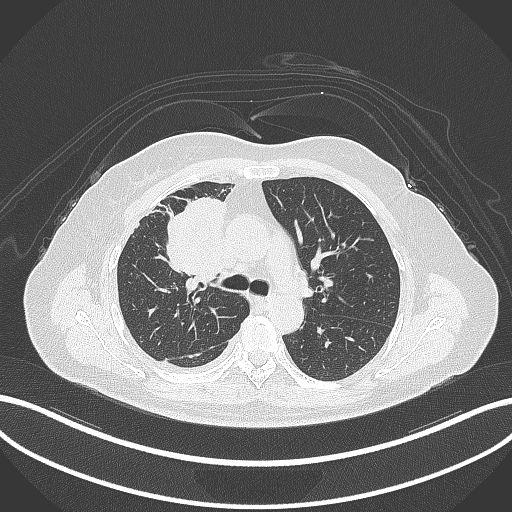
Chest CT, one axial slice. Reconstruction kernel B70f. Lung window (W 1500 / L -600 HU). 512 × 512 image matrix, field of view 400 × 400 mm. Patient: female, 52 years. From the clinical record (not read from this slice): clinical TNM (as recorded): T3 N1 M1.
Annotated regions visible in this slice (bounding box drawn by a radiologist):
- lung tumour (recorded histology: adenocarcinoma): bounding box [x1, y1, x2, y2] px = [162, 192, 234, 286]